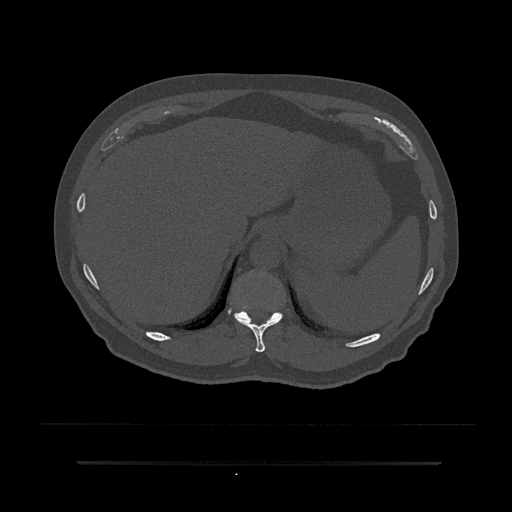
CT including the spine, one axial slice. Slice 302 of 797 in the series (ordered by position). 120 kVp. Bone window (W 1800 / L 400 HU). 0.5 mm slice thickness. 512 × 512 image matrix, field of view 464 × 464 mm. Male patient, age 59 years. From the clinical record (not read from this slice): primary cancer: bile ducts.
Outlined on this slice (semi-automatic segmentation, software-assisted and operator-edited):
- T10 vertebra: bounding box <235,316,282,353> (left, top, right, bottom; pixels)
- T11 vertebra: <233,302,283,322>